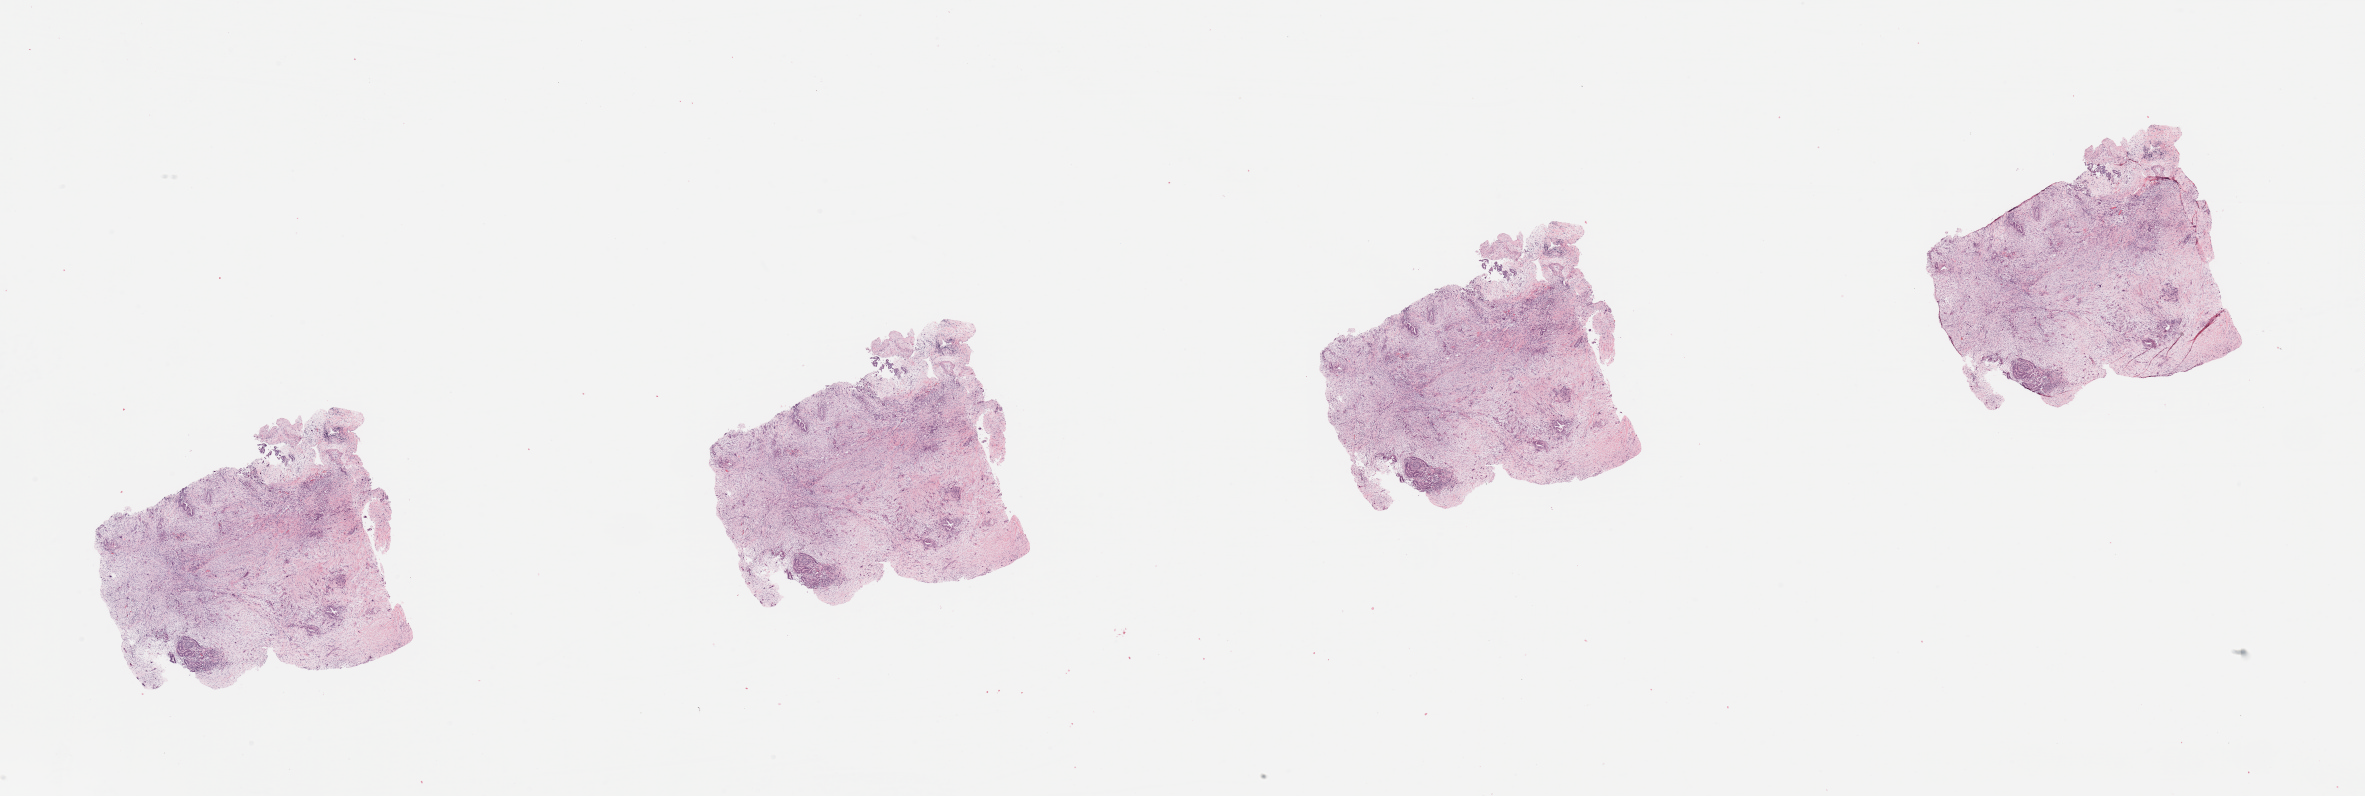
H&E whole-slide image — low-resolution overview of the scanned area, about 37.4 x 12.6 mm (acquisition: 20x scan); tumour tissue sample, sampled site: pancreas. 68-year-old female patient. Histologic grade: G2 (moderately differentiated). Slide review estimates, as recorded: tumour nuclei 50%, necrosis 0%.
AJCC pathologic stage: IIB. Primary tumour site (as recorded): head. Diagnosis: Infiltrating duct carcinoma, NOS.